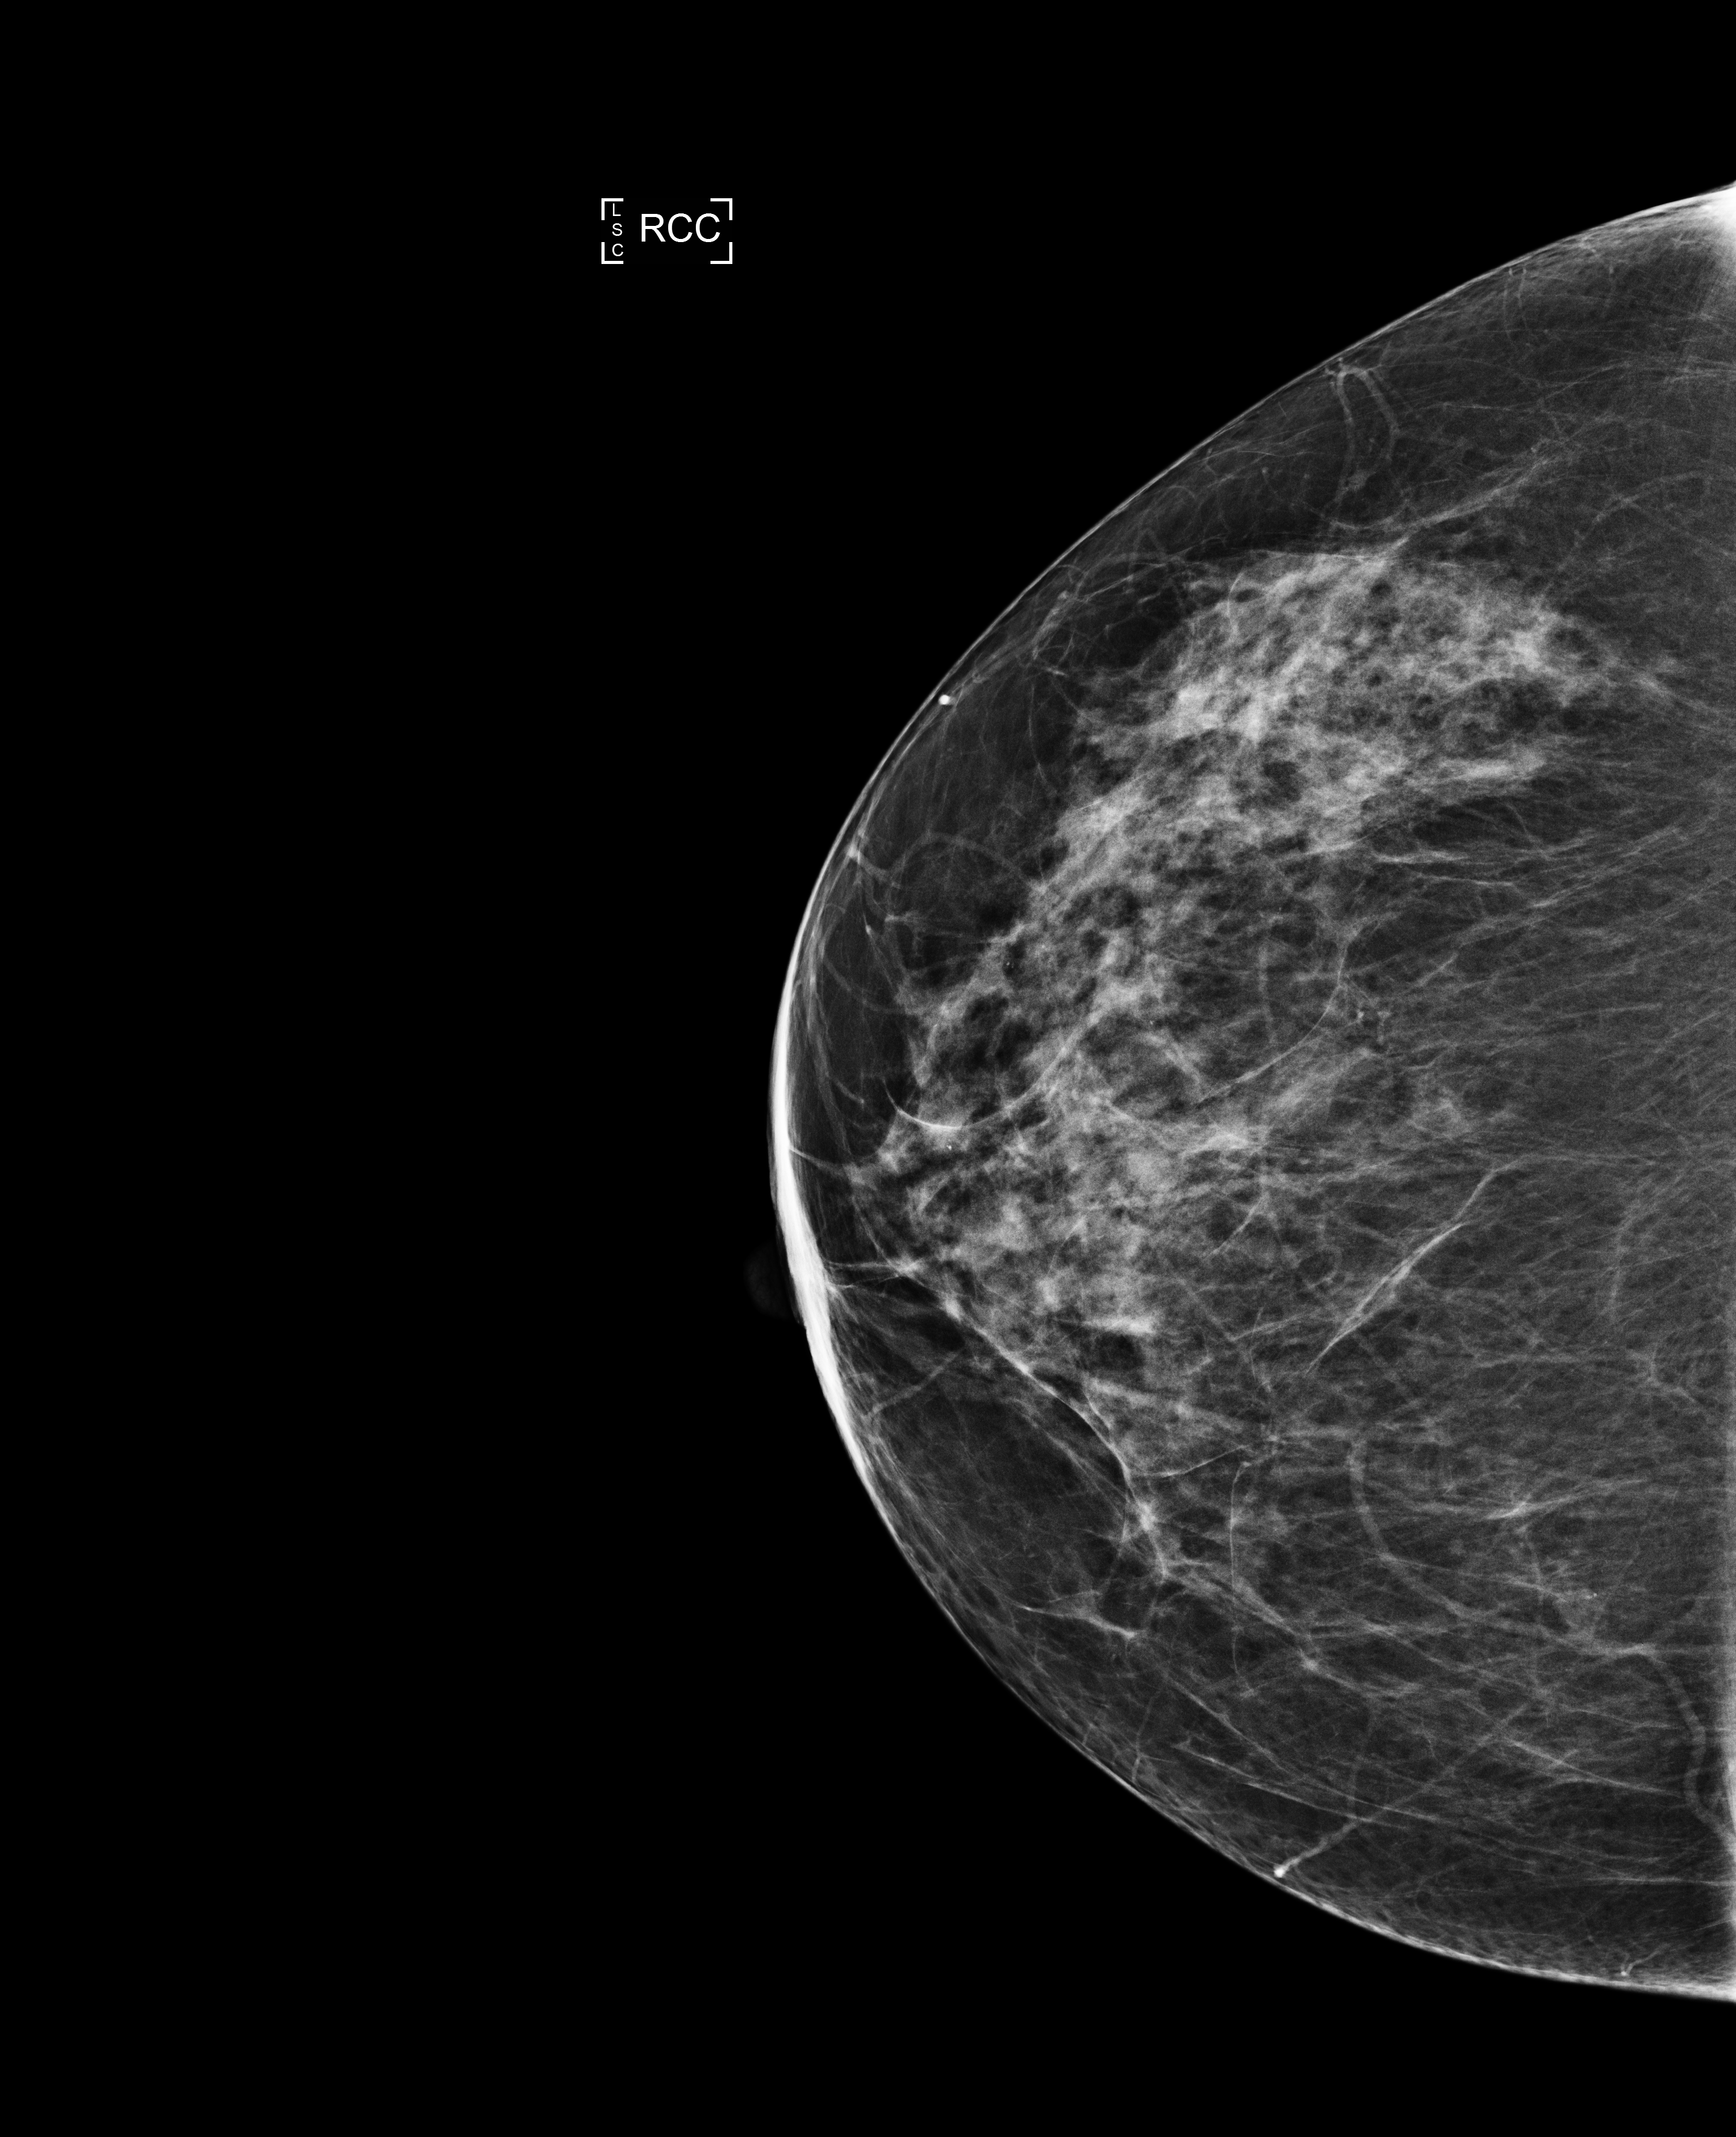
Full-field digital mammogram (FFDM), right breast, cranio-caudal projection, screening examination, compressed breast thickness 64 mm, system: Selenia Dimensions. Female patient, age 57 years.
- breast density at the screening exam (both breasts): heterogeneously dense (BI-RADS density category c)
- final BI-RADS assessment for this screening round (tomosynthesis exam, both breasts): category 2
- recall: no recall after this screen